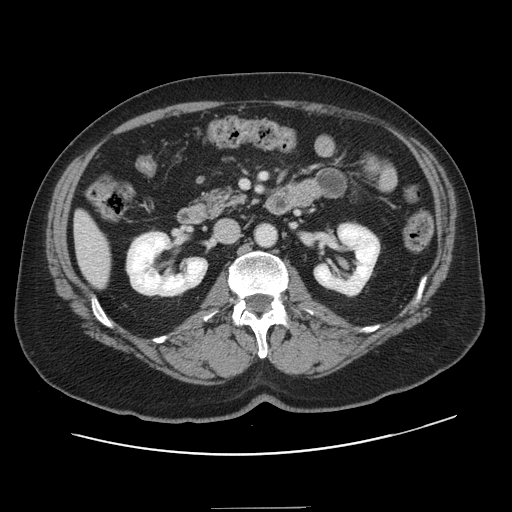
Contrast-enhanced abdominal CT, one axial slice. Position 51 of 143 along the scan axis. Intravenous contrast given. Soft-tissue window (W 400 / L 40 HU). 2.5 mm slice thickness. 512 × 512 image matrix, field of view 402 × 402 mm. Male patient, age 62 years. From the clinical record (not read from this slice): diagnosis: colorectal cancer liver metastases, imaged before liver resection; multiple liver metastases: yes; largest metastasis: 2.7 cm; disease in both lobes: no.
Outlined on this slice (expert manual segmentation):
- liver: bounding box (x1, y1, x2, y2) in pixels: (76, 214, 110, 287)